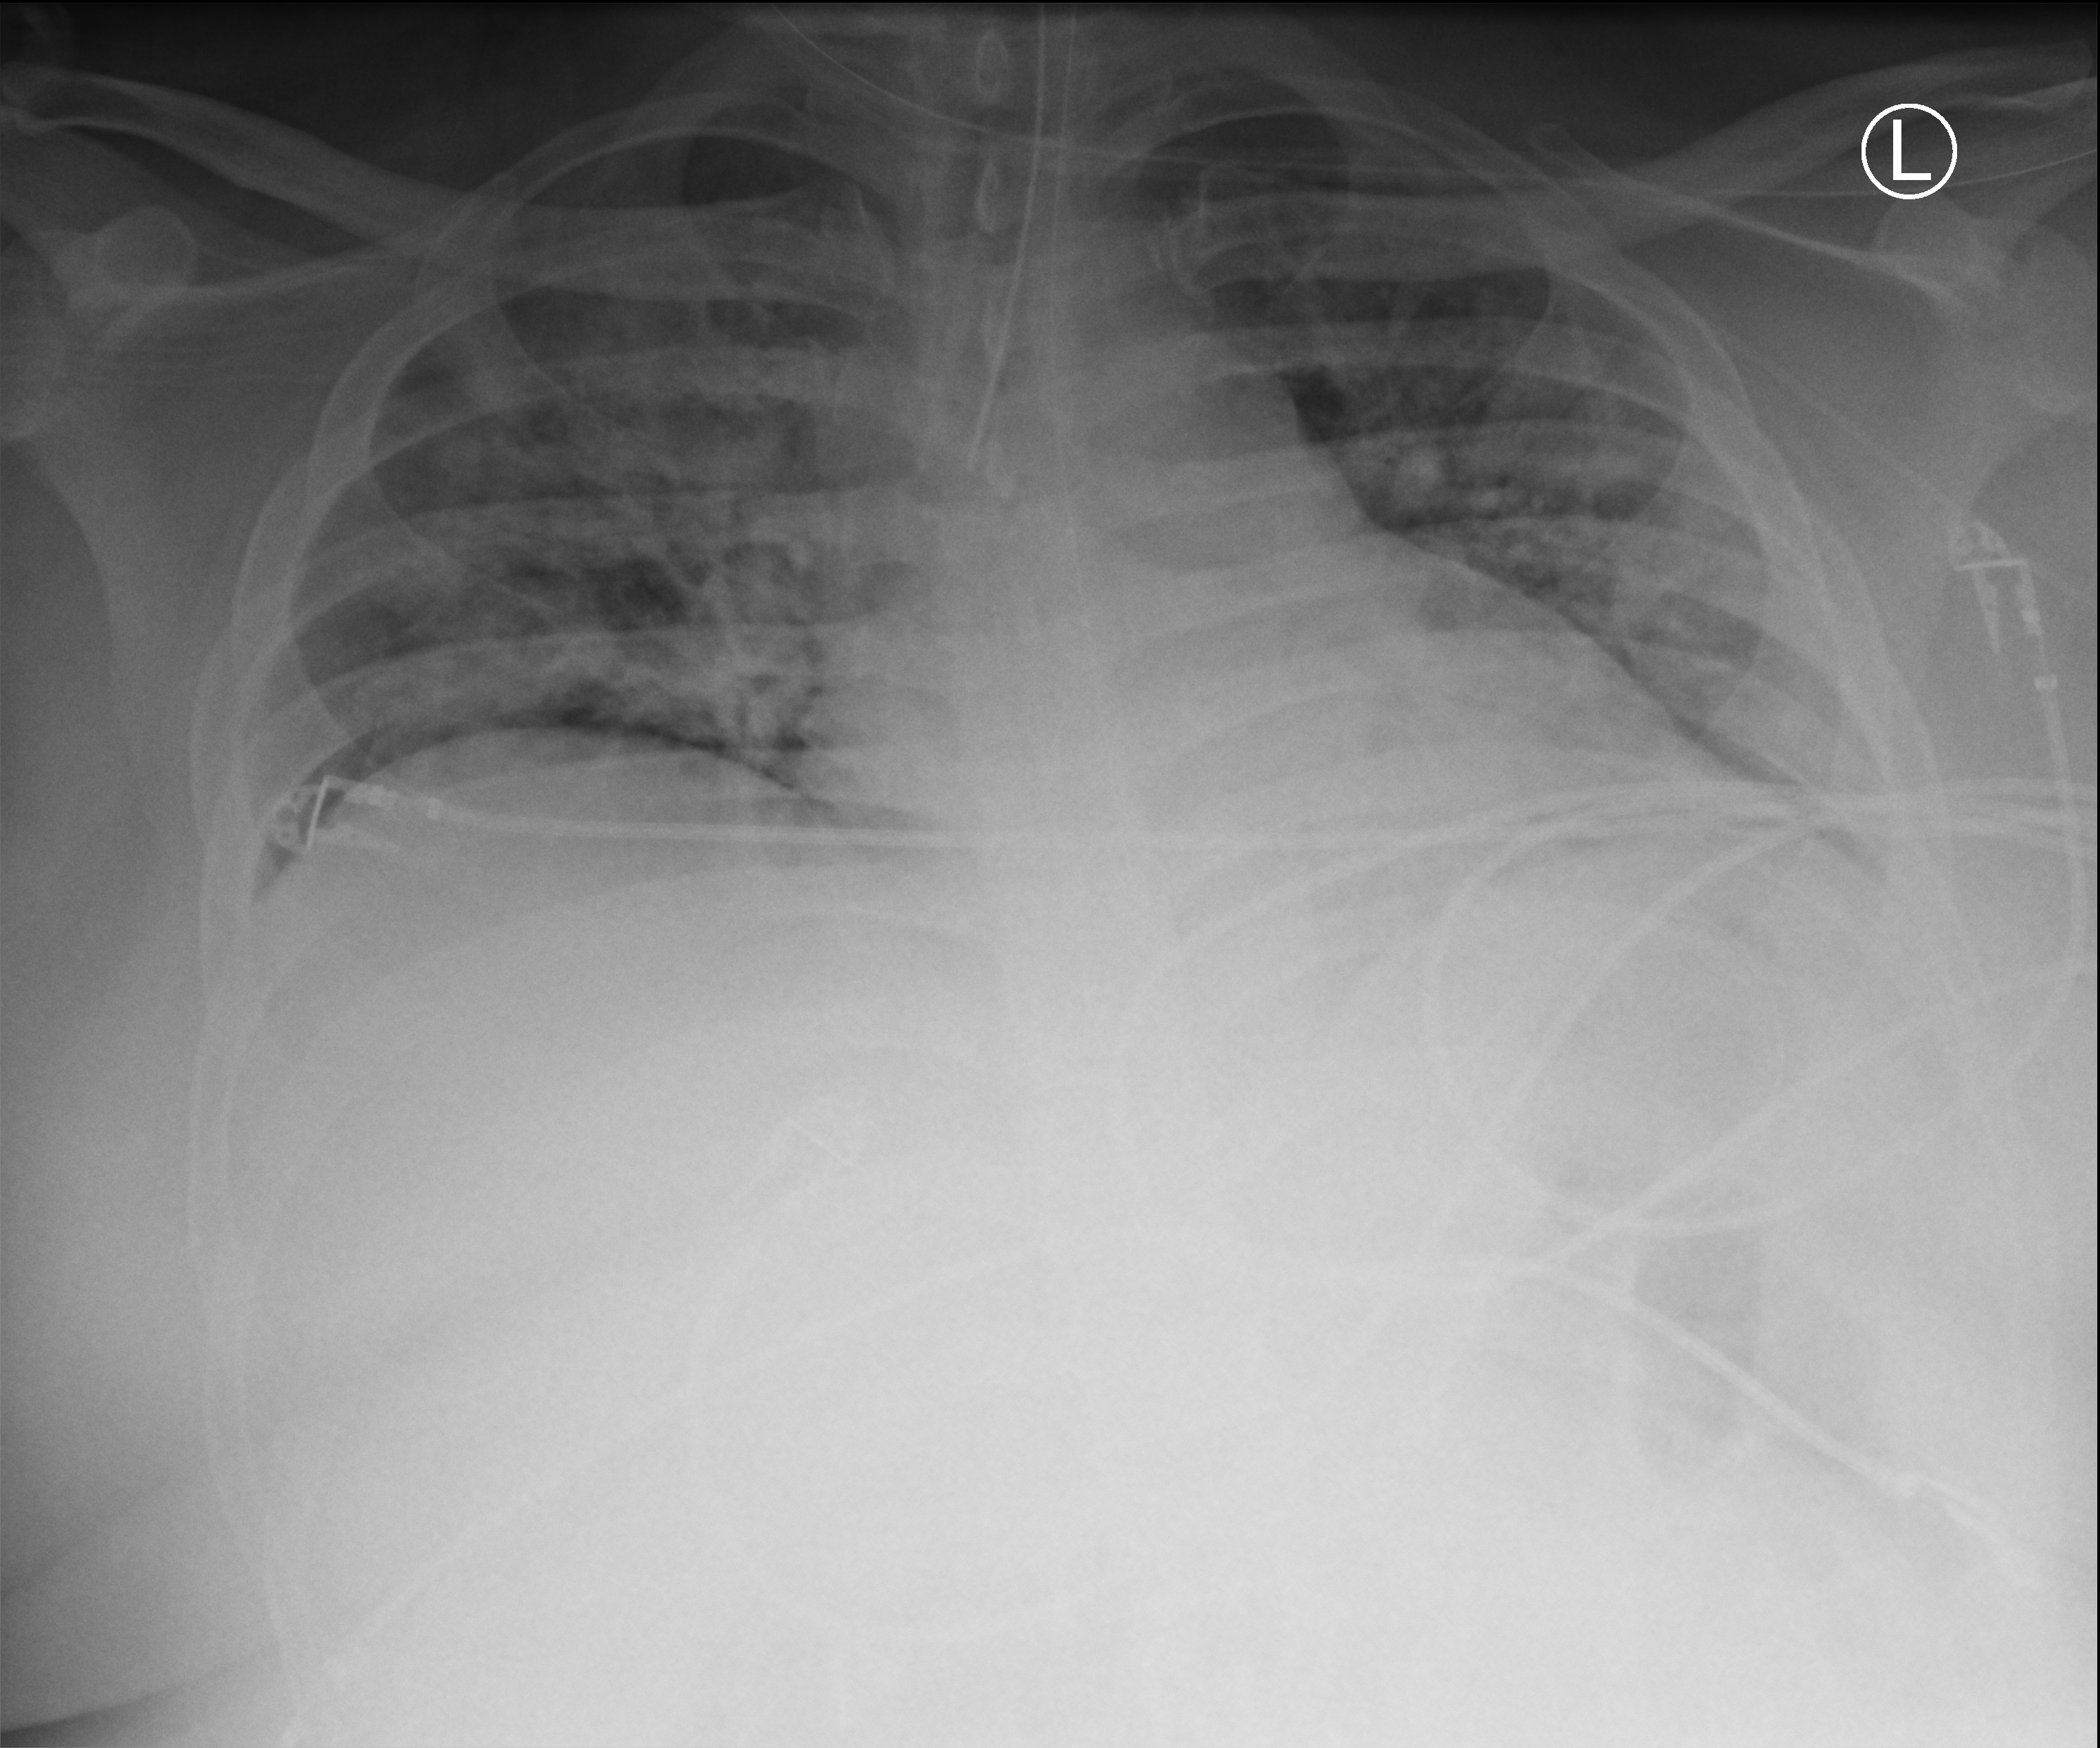
Chest X-ray (portable), anteroposterior (AP) projection. Patient hospitalised with COVID-19; male, aged 18–59 years.
Admission-level facts for this patient (not findings on this image; timing relative to this image not recorded): diabetes (admission record): yes.